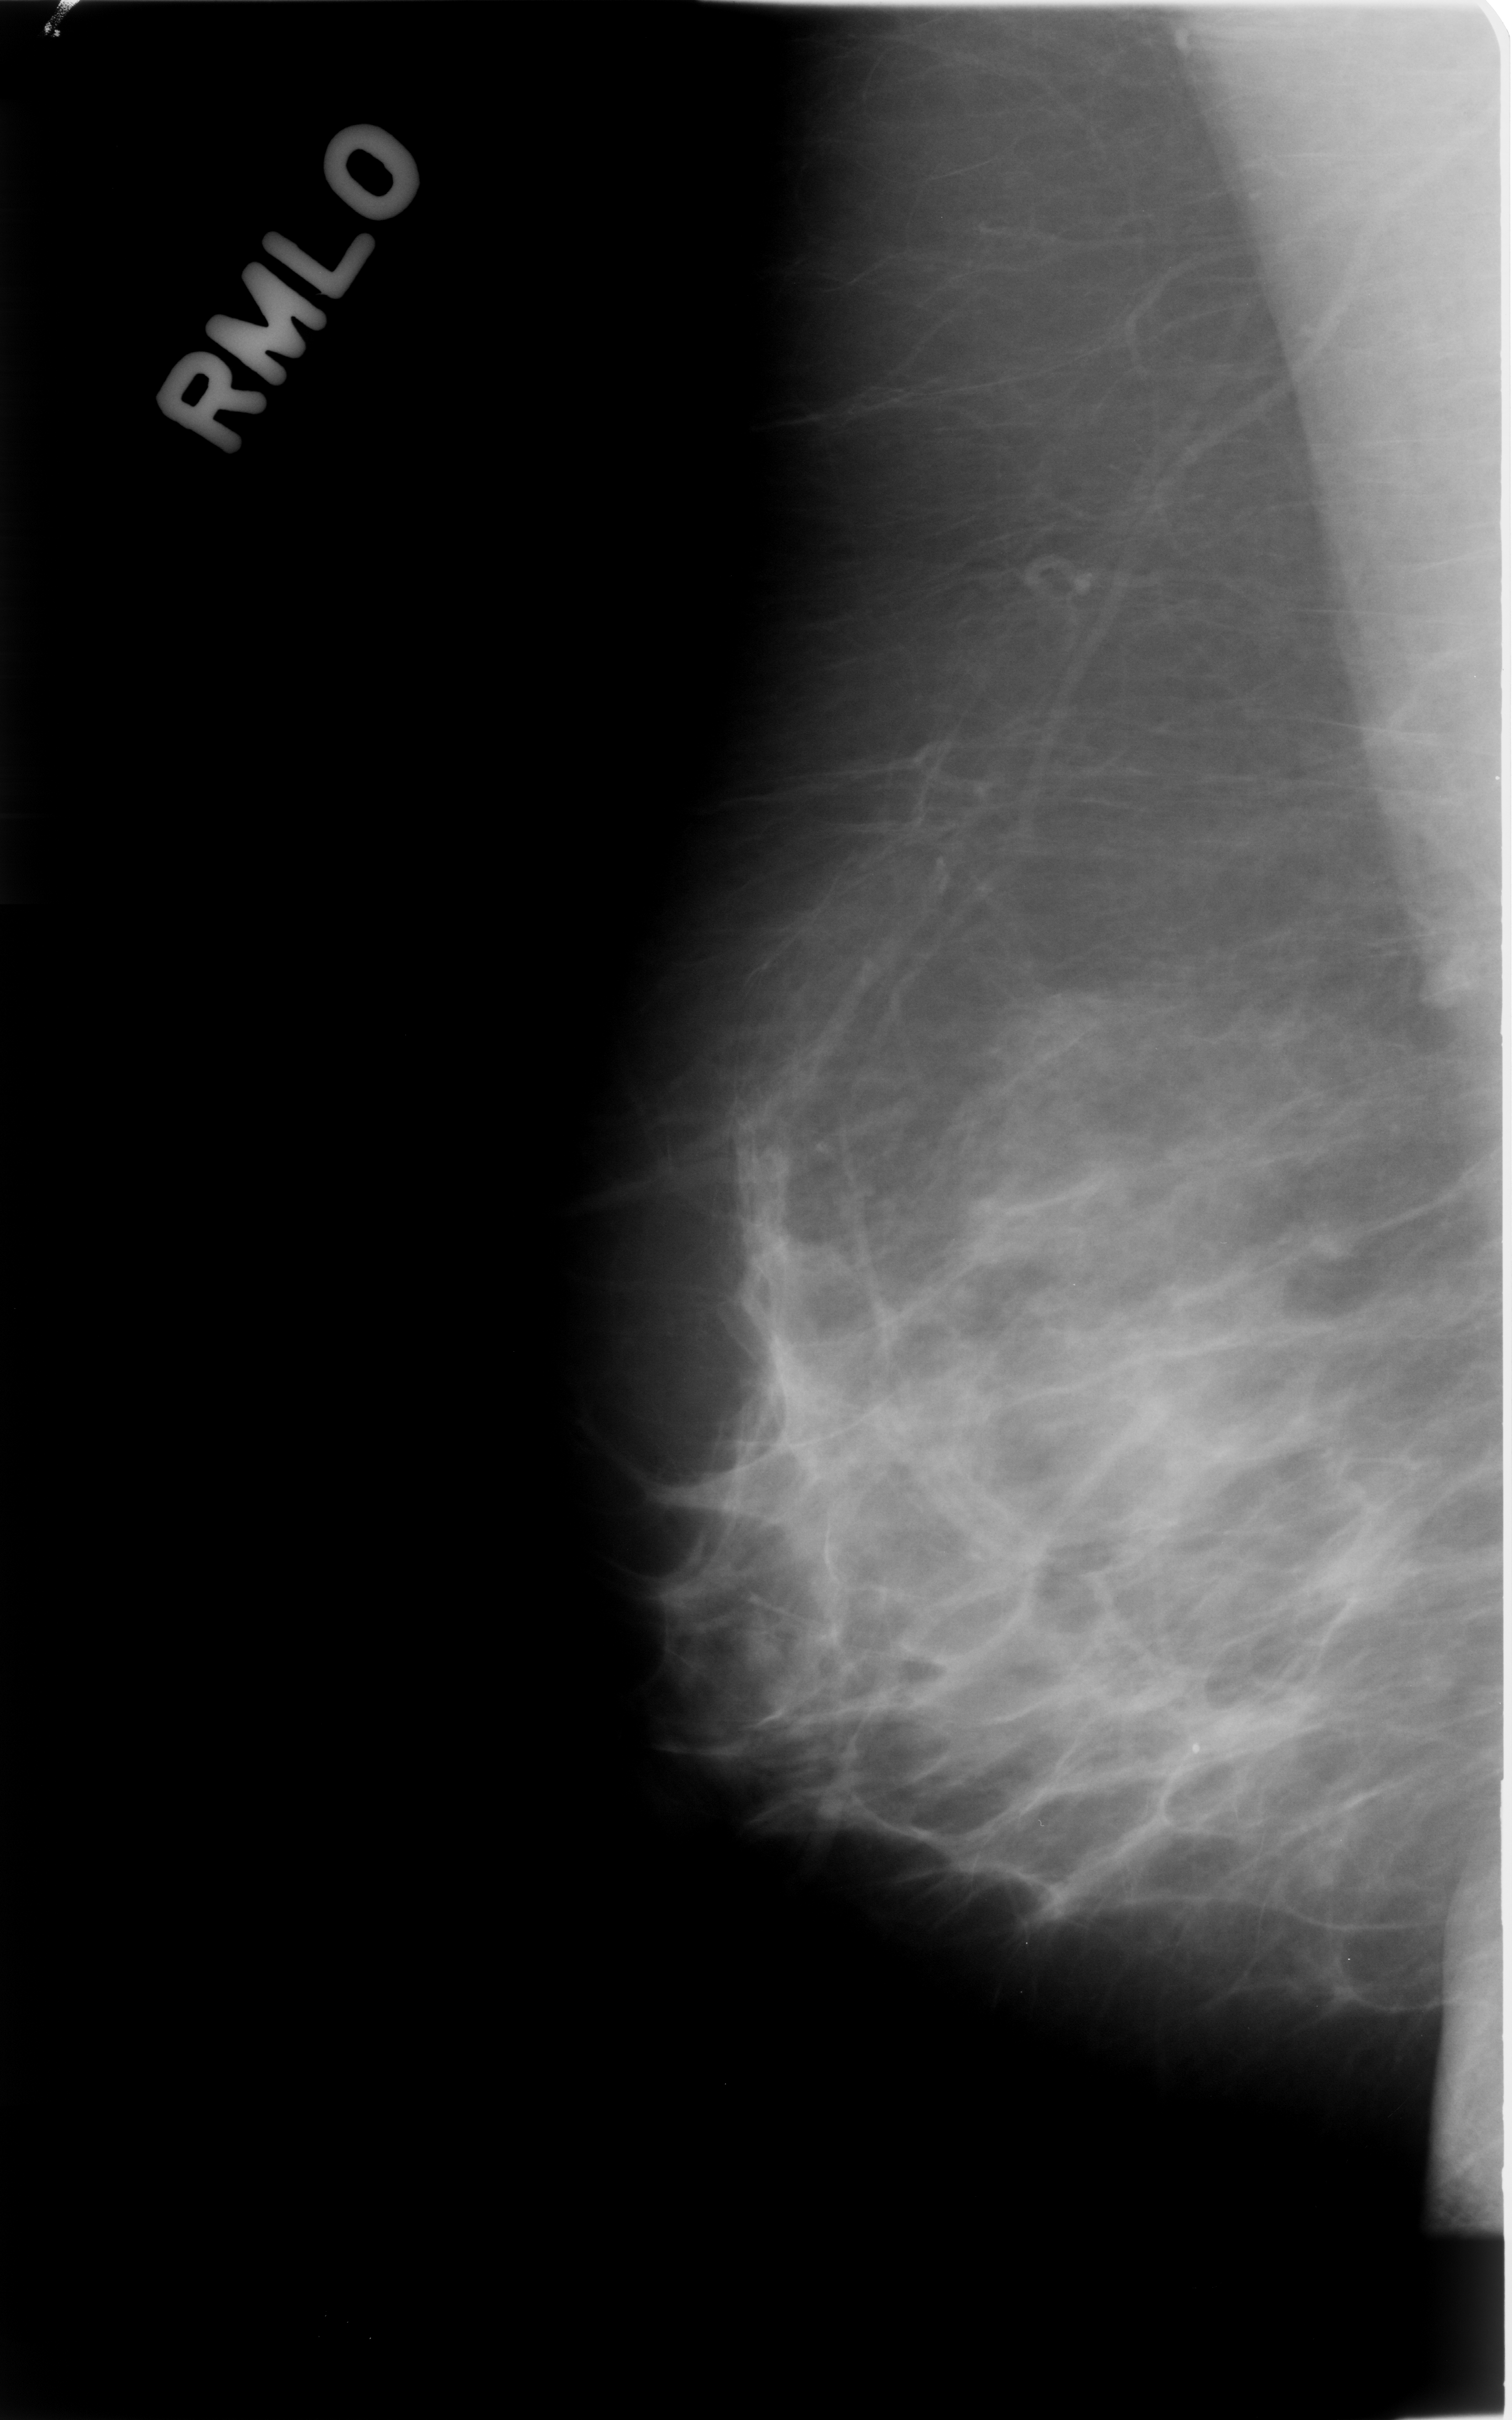
Scanned film-screen mammogram; right breast; MLO view; breast composition: scattered fibroglandular densities (BI-RADS density category 2 of 4).
Abnormality record for this image: mass, shape lobulated, margins microlobulated; BI-RADS assessment category 3; benign; no additional work-up was recommended (benign without callback).